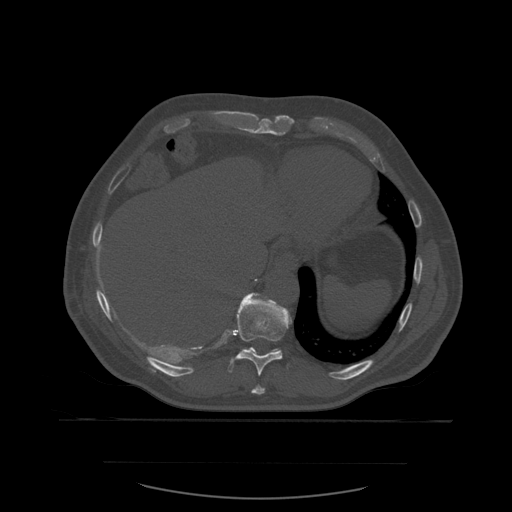
CT including the spine, one axial slice. Bone window (W 1800 / L 400 HU). 1.25 mm slice thickness. 512 × 512 image matrix, field of view 479 × 479 mm. Patient age 71 years. From the clinical record (not read from this slice): primary cancer: lung; vertebrae with lytic lesions (as recorded): T1, T2, L5, S1.
Outlined on this slice (semi-automatically segmented with operator editing):
- T10 vertebra: bounding box (x1, y1, x2, y2) in pixels: (228, 293, 293, 376)
- T11 vertebra: (245, 348, 279, 352)
- T9 vertebra: (252, 385, 266, 395)